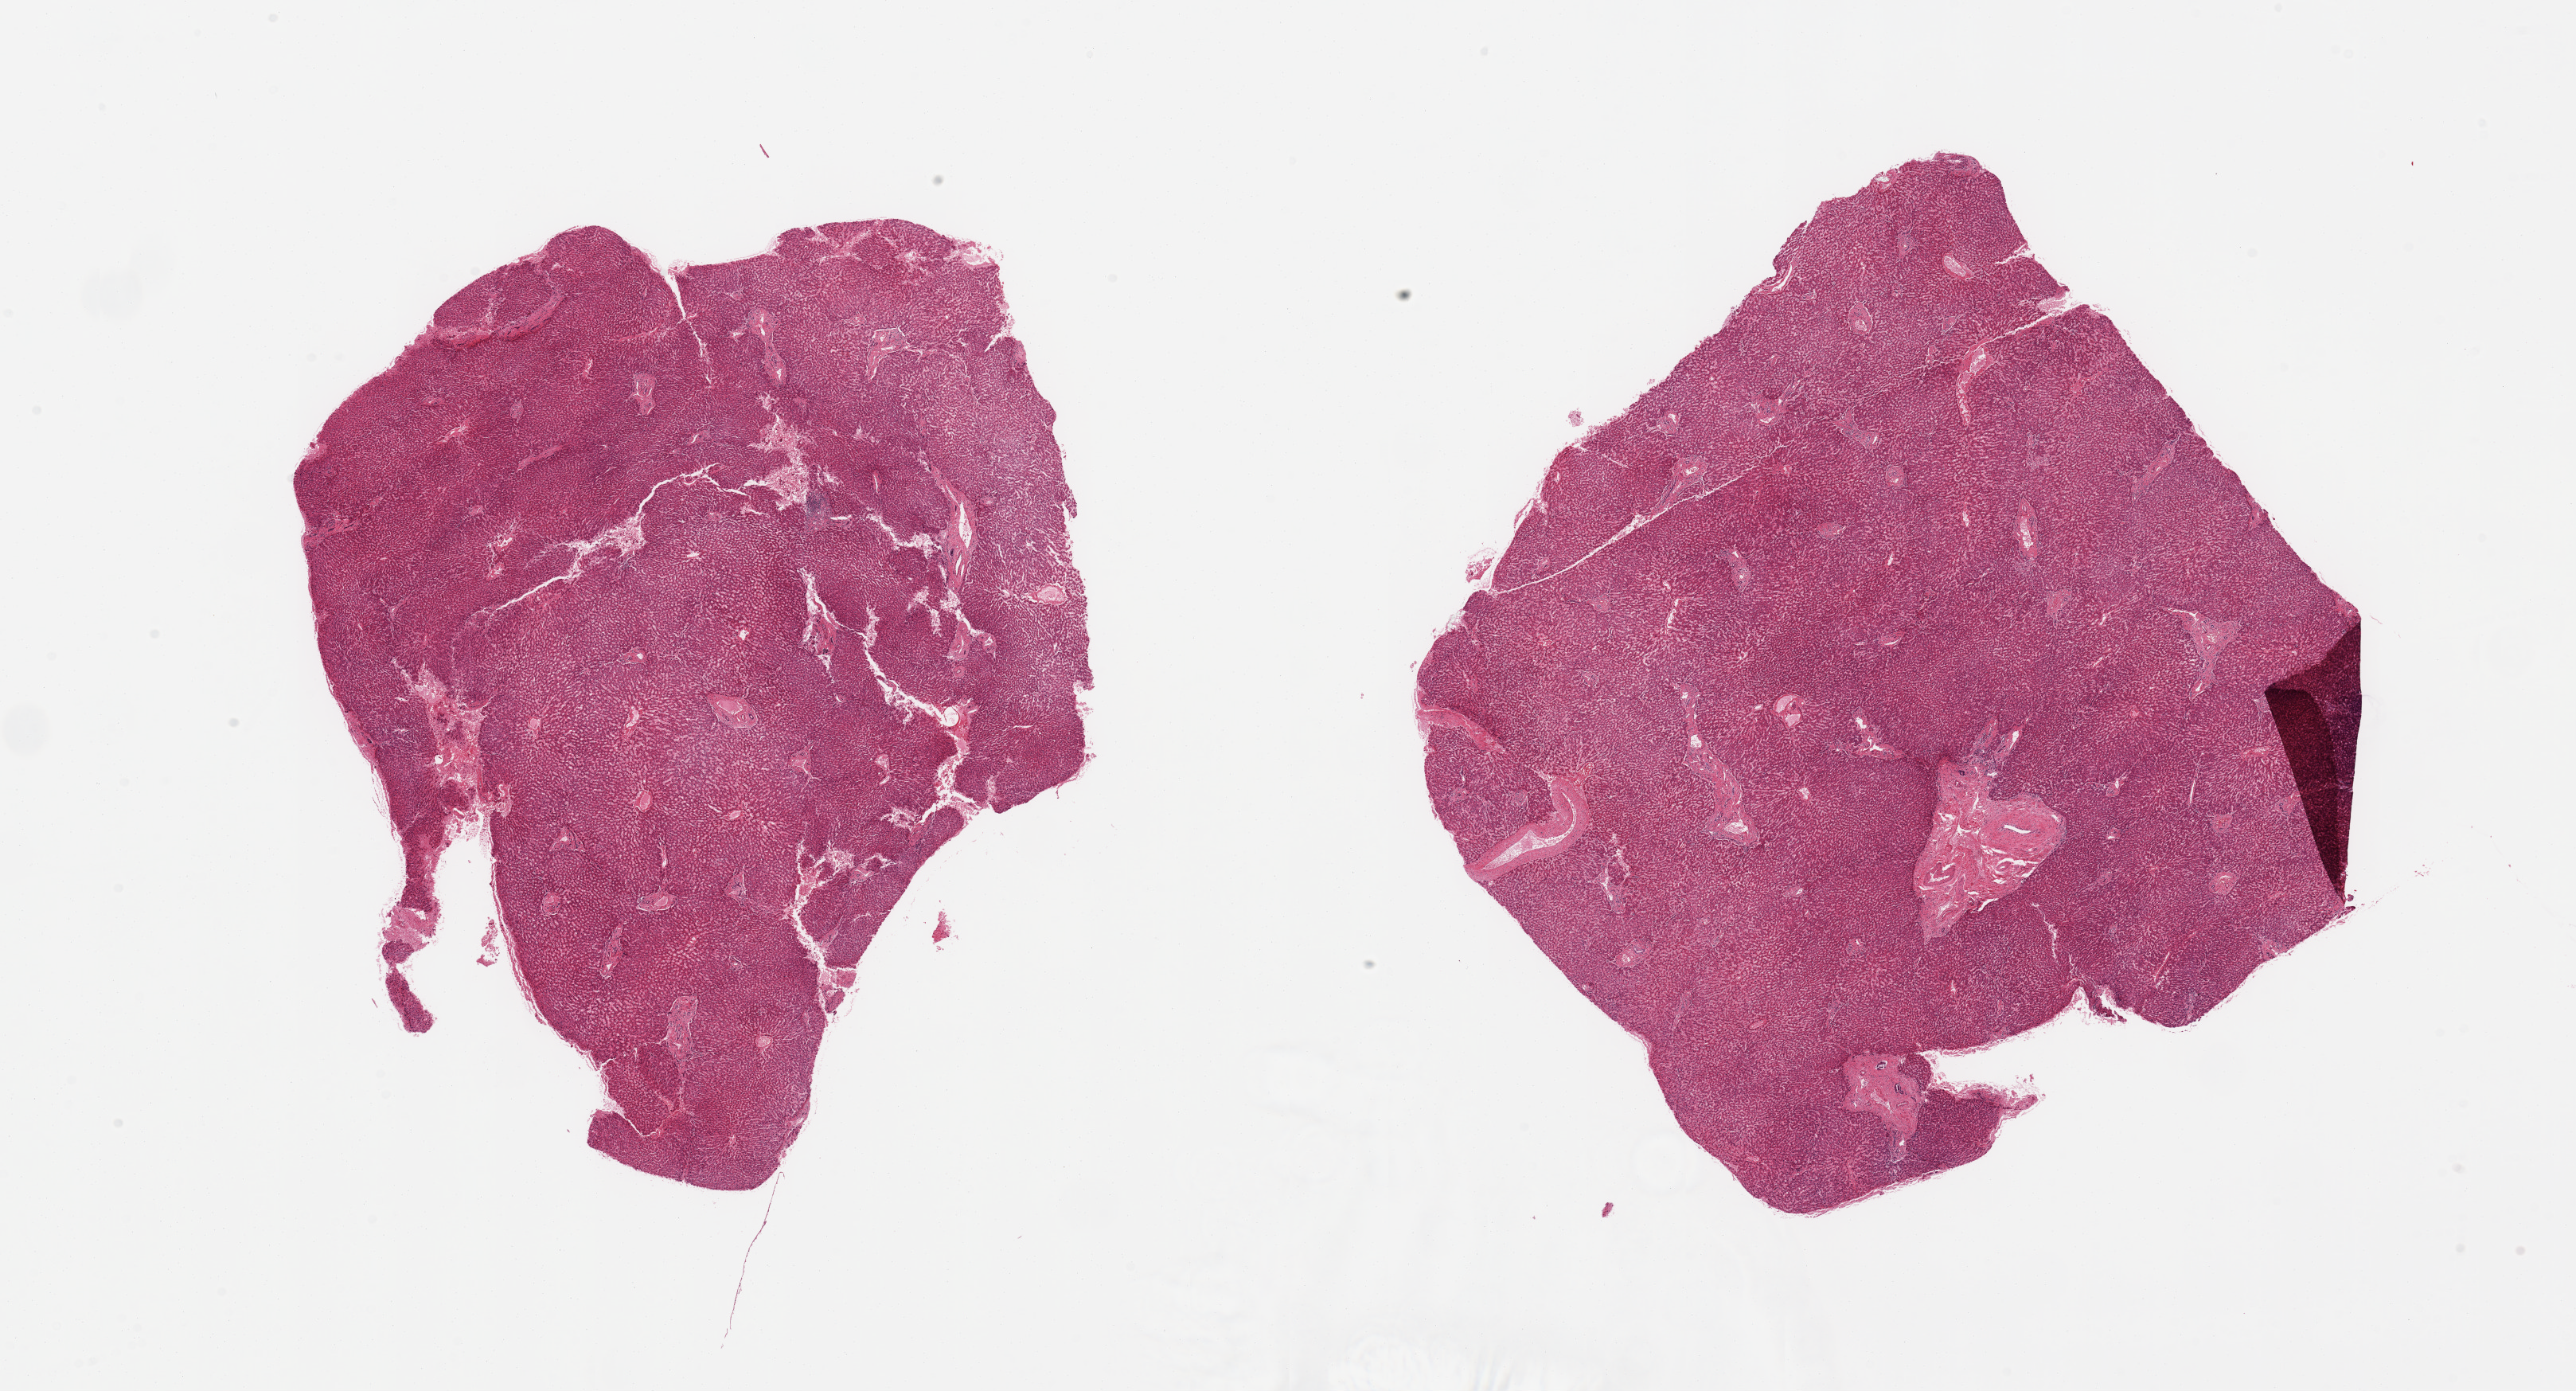
Digitized hematoxylin and eosin (H&E)-stained section, brightfield — whole scanned area (about 25.6 x 13.8 mm, acquisition: 20x scan) shown as a low-resolution overview; PAXgene-fixed, paraffin-embedded tissue; section of liver (target tissue); donor tissue sample.
Pathologist's review note for this sample: 2 pieces, mild congestion.